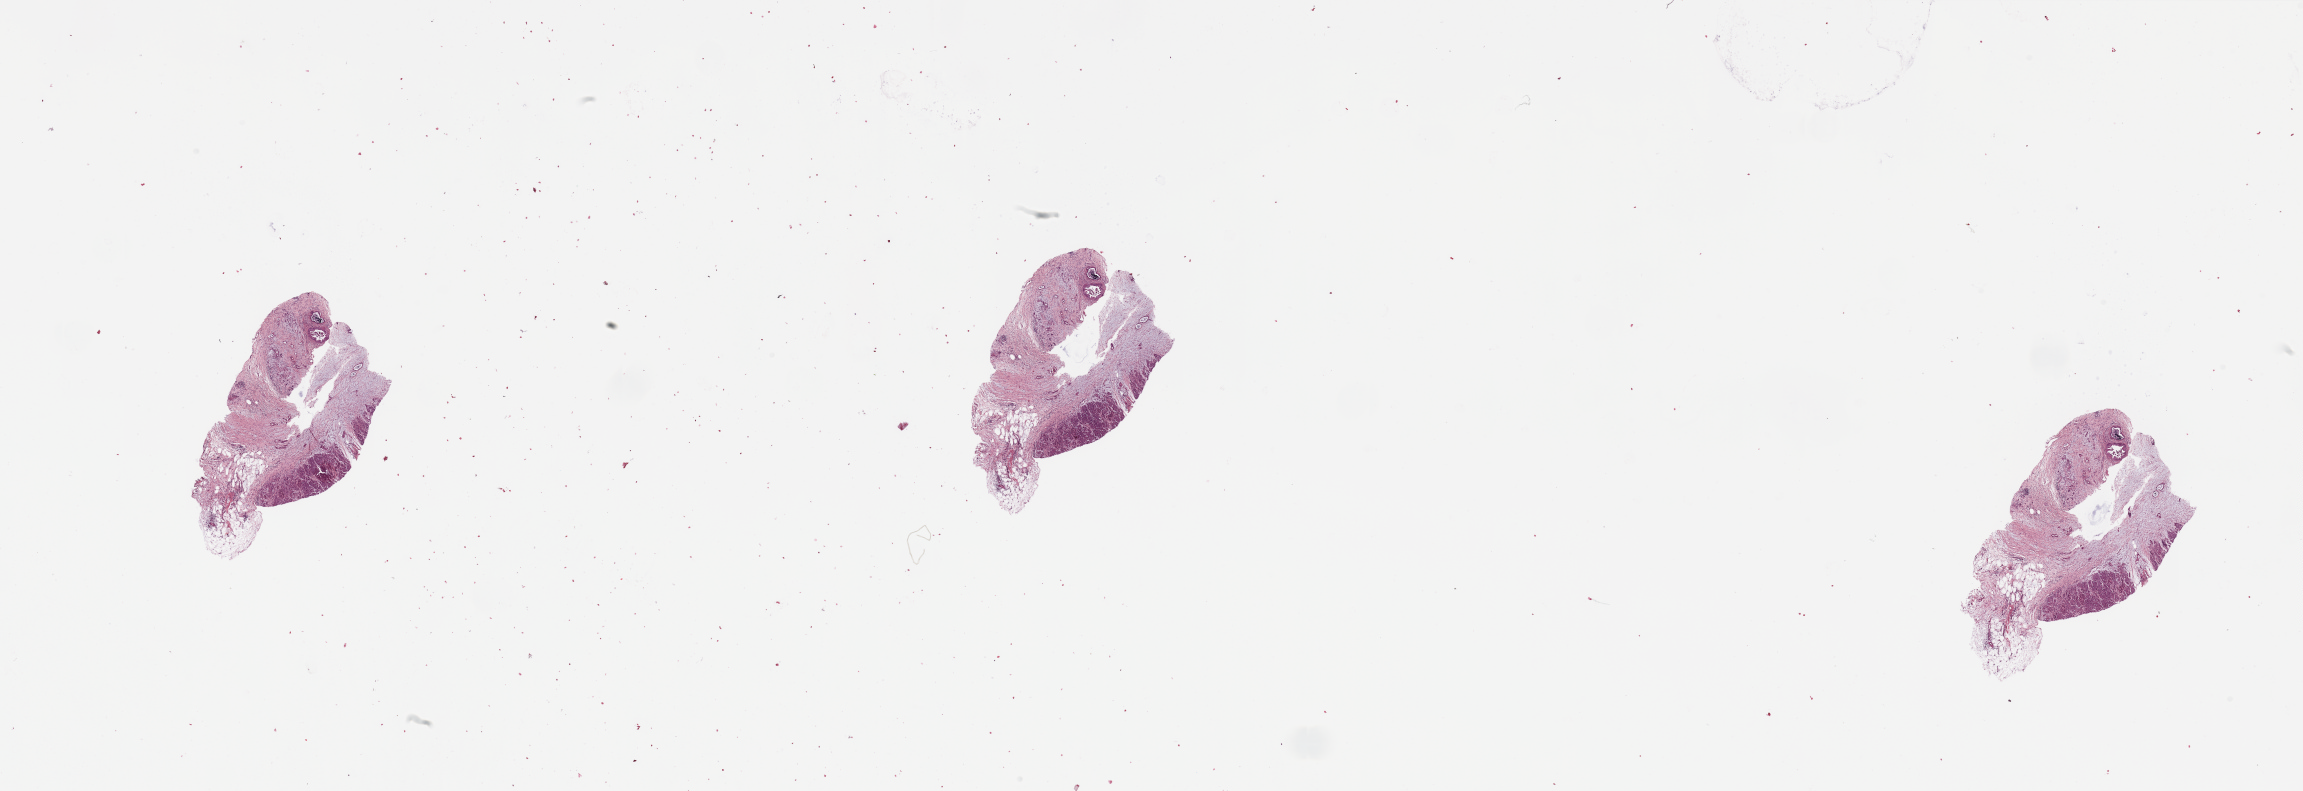
Digitized Hematoxylin and eosin (H&E) stained tissue section (whole slide) — low-resolution overview of the scanned area, about 36.4 x 12.5 mm (acquisition: 20x scan), tumour tissue sample, sampled site: pancreas. 65-year-old male patient. Histologic grade: G2 (moderately differentiated). Pathologist review of this section (percent, as recorded): tumour nuclei 10%, necrosis 2%.
- AJCC pathologic stage: IV
- histologic diagnosis: Infiltrating duct carcinoma, NOS
- primary tumour site (as recorded): head